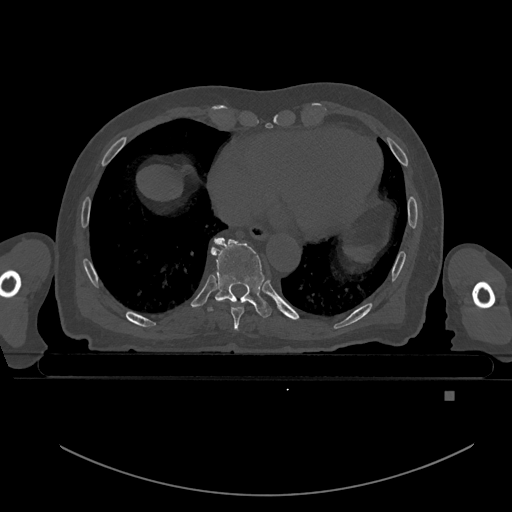
CT including the spine, one axial slice. Position 165 of 969 along the scan axis. Bone window (W 1800 / L 400 HU). 0.5 mm slice thickness. 512 × 512 image matrix. Patient: male, 82 years. From the clinical record (not read from this slice): primary cancer: prostate; vertebrae with lytic lesions (as recorded): T11, T9, T8, T2.
Outlined on this slice (semi-automatic segmentation, software-assisted and operator-edited):
- T8 vertebra: box from (x=216, y=299) to (x=249, y=331) px
- T9 vertebra: (x=209, y=237)–(x=272, y=318)